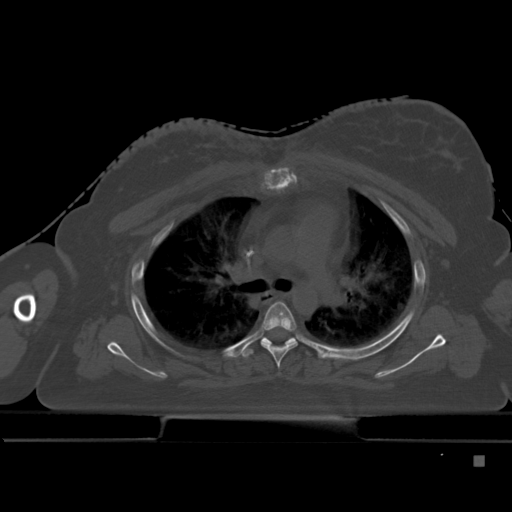
CT including the spine, one axial slice. Position 328 of 495 along the scan axis. Bone window (W 1800 / L 400 HU). 1.5 mm slice thickness. 512 × 512 image matrix, field of view 404 × 404 mm. Patient: female, 33 years. Case-level facts recorded for this patient, not image findings: primary cancer: breast.
Structures marked on this image (semi-automatic segmentation, software-assisted and operator-edited):
- T4 vertebra: bounding box <262,302,297,369> (left, top, right, bottom; pixels)
- T5 vertebra: <242,336,311,358>